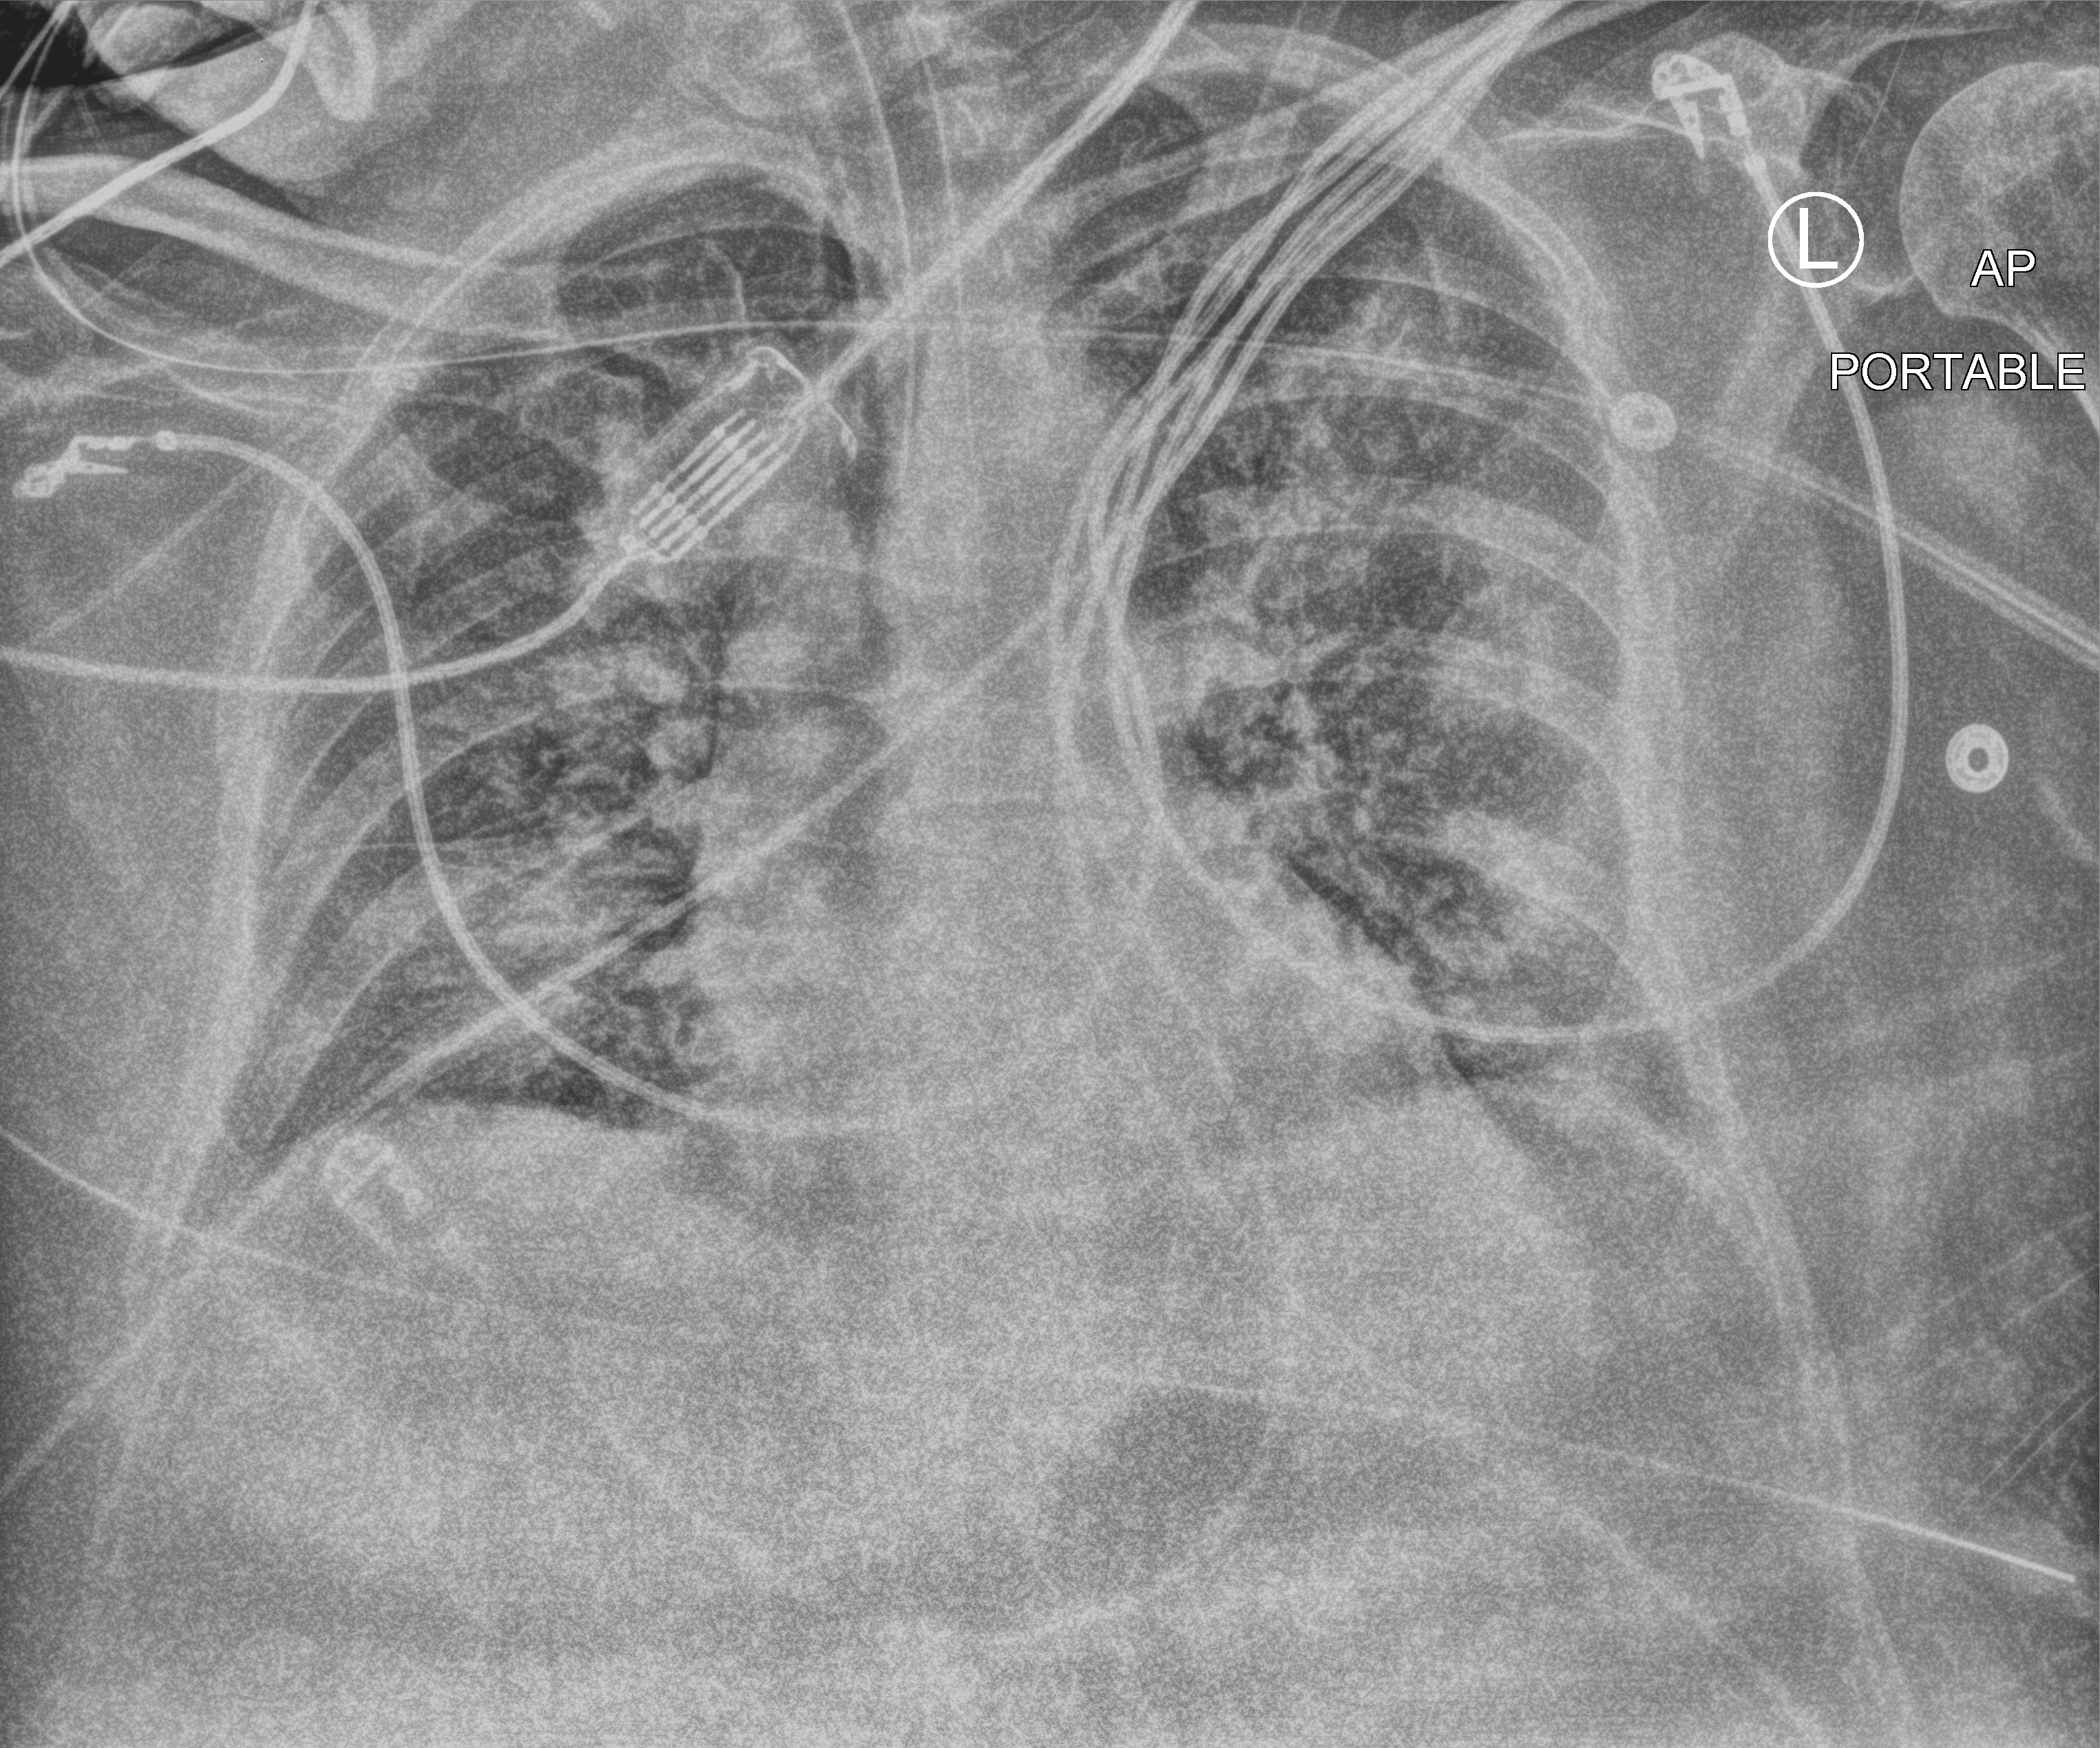
Chest X-ray (portable). Patient hospitalised with COVID-19; male, aged 60–74 years.
From the hospital-stay record, not from the radiograph (when in the stay this image was taken is not recorded):
- mechanically ventilated during this hospital stay: yes